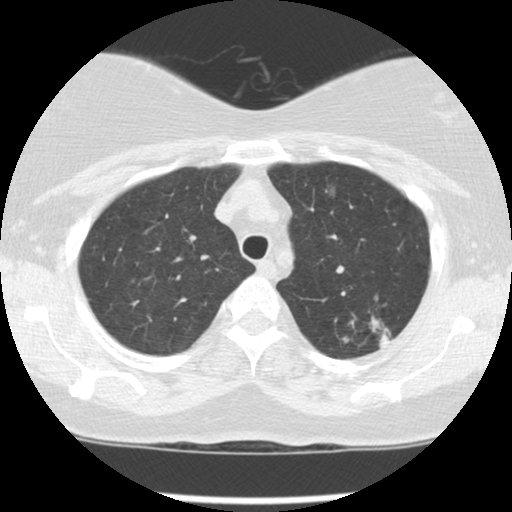
Low-dose screening chest CT, one axial slice. Slice 105 of 127 in the series (ordered by position). Reconstruction kernel STANDARD. 120 kVp. Lung window (W 1500 / L -600 HU). 2.5 mm slice thickness. 512 × 512 image matrix, field of view 310 × 310 mm.
Outlined on this slice (expert manual segmentation):
- lesion 1 (tumor, upper lobe of left lung): bounding box <367,315,391,347> (left, top, right, bottom; pixels)